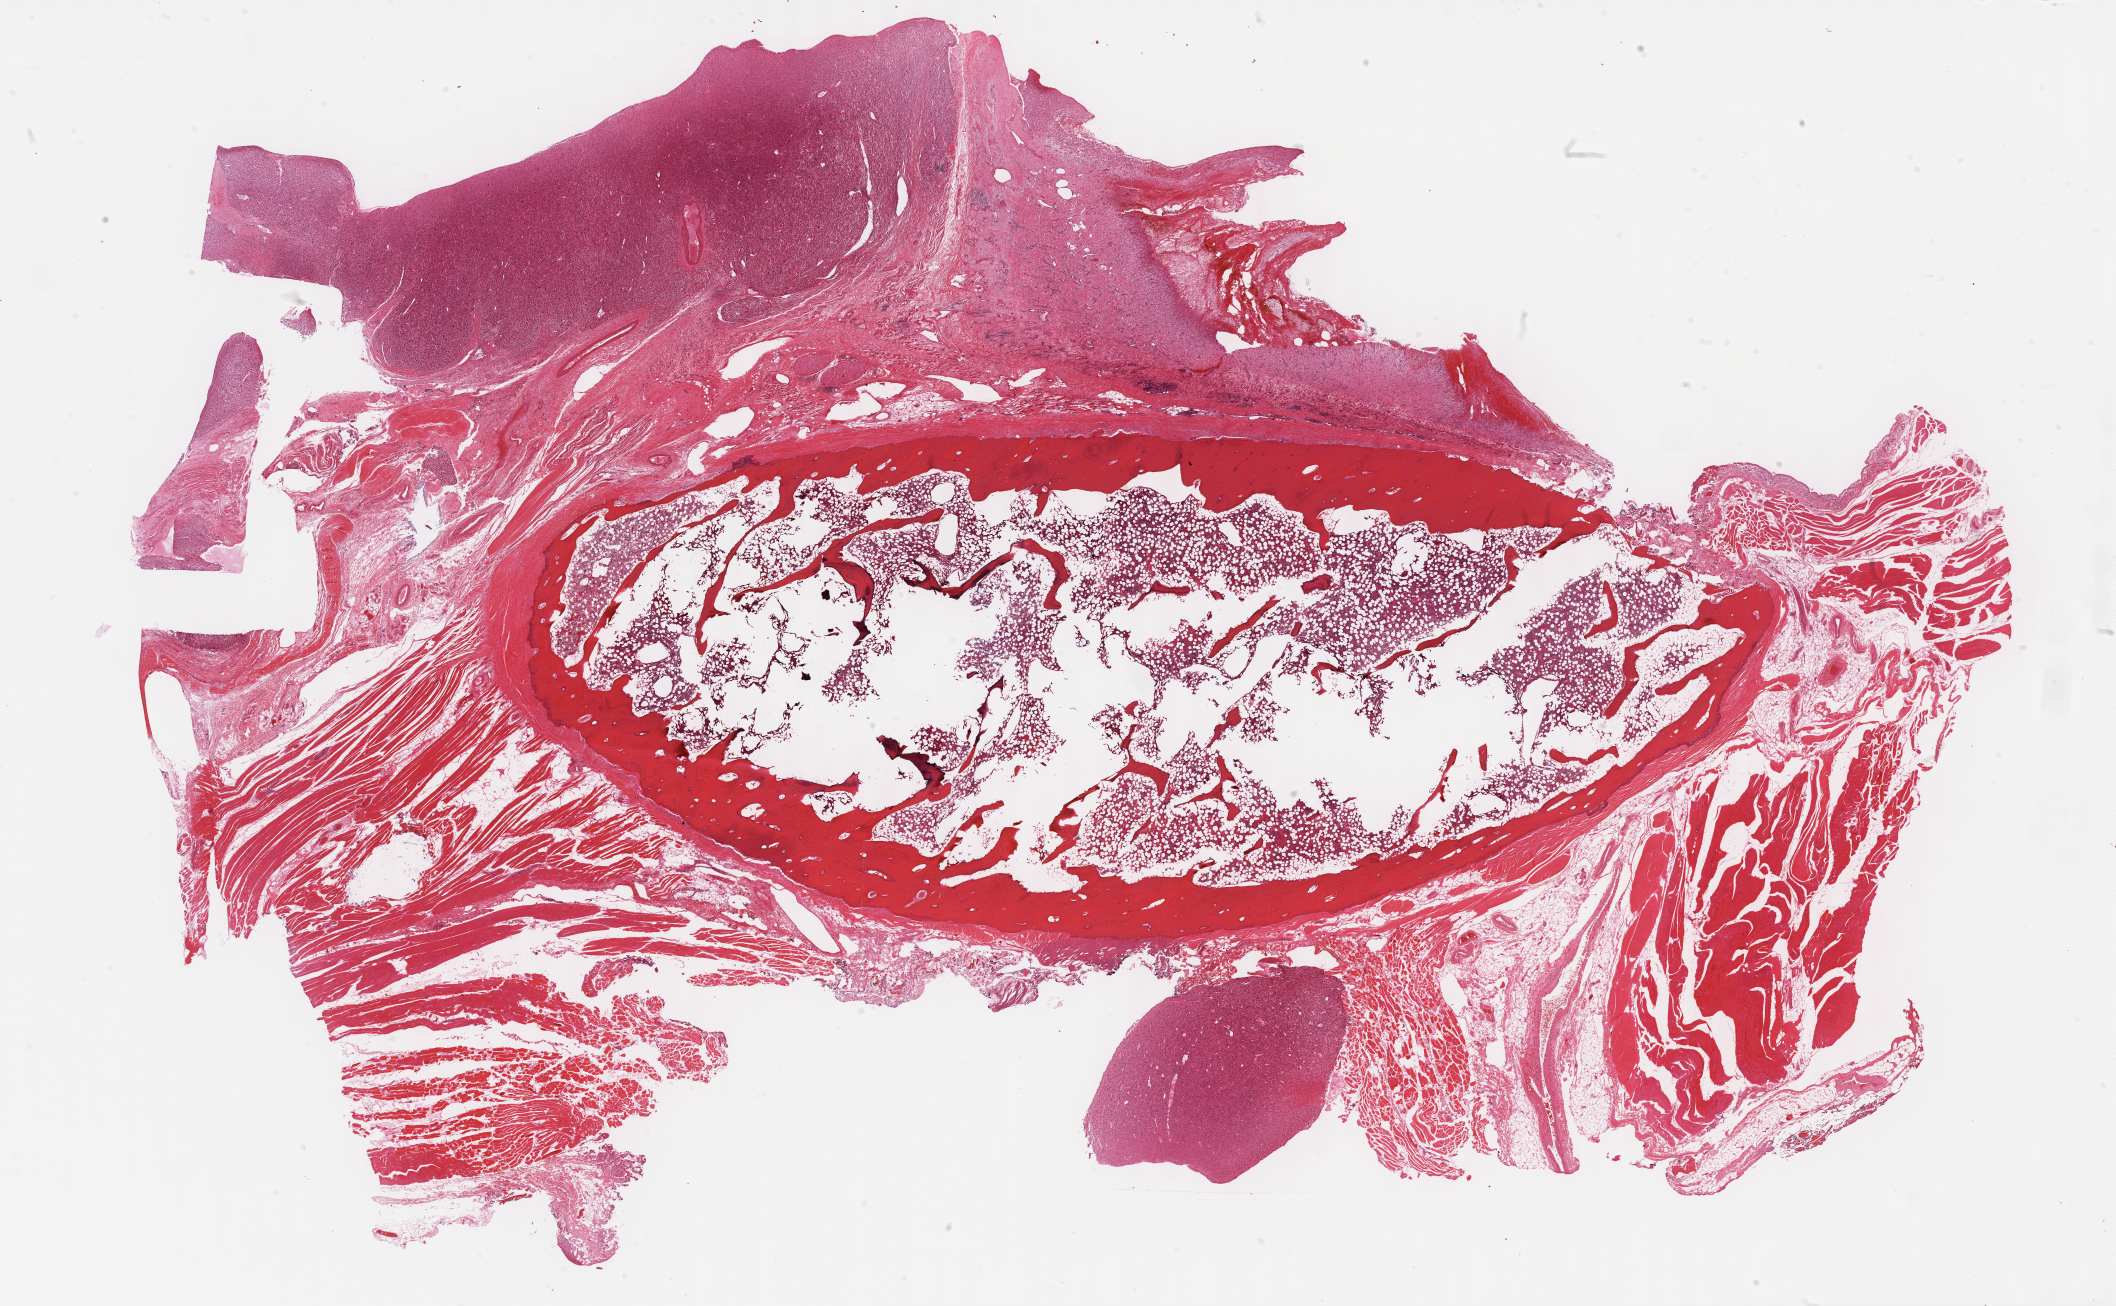
Whole-slide histology image, H&E-stained — low-resolution overview of the scanned area, about 34.2 x 21.1 mm (acquisition: 40x scan). Formalin-fixed paraffin-embedded (FFPE) diagnostic section. Primary tumour sample from the connective, subcutaneous and other soft tissues. Patient: female, age at initial diagnosis 49 years.
Diagnosis: Undifferentiated sarcoma (connective, subcutaneous and other soft tissues of thorax).